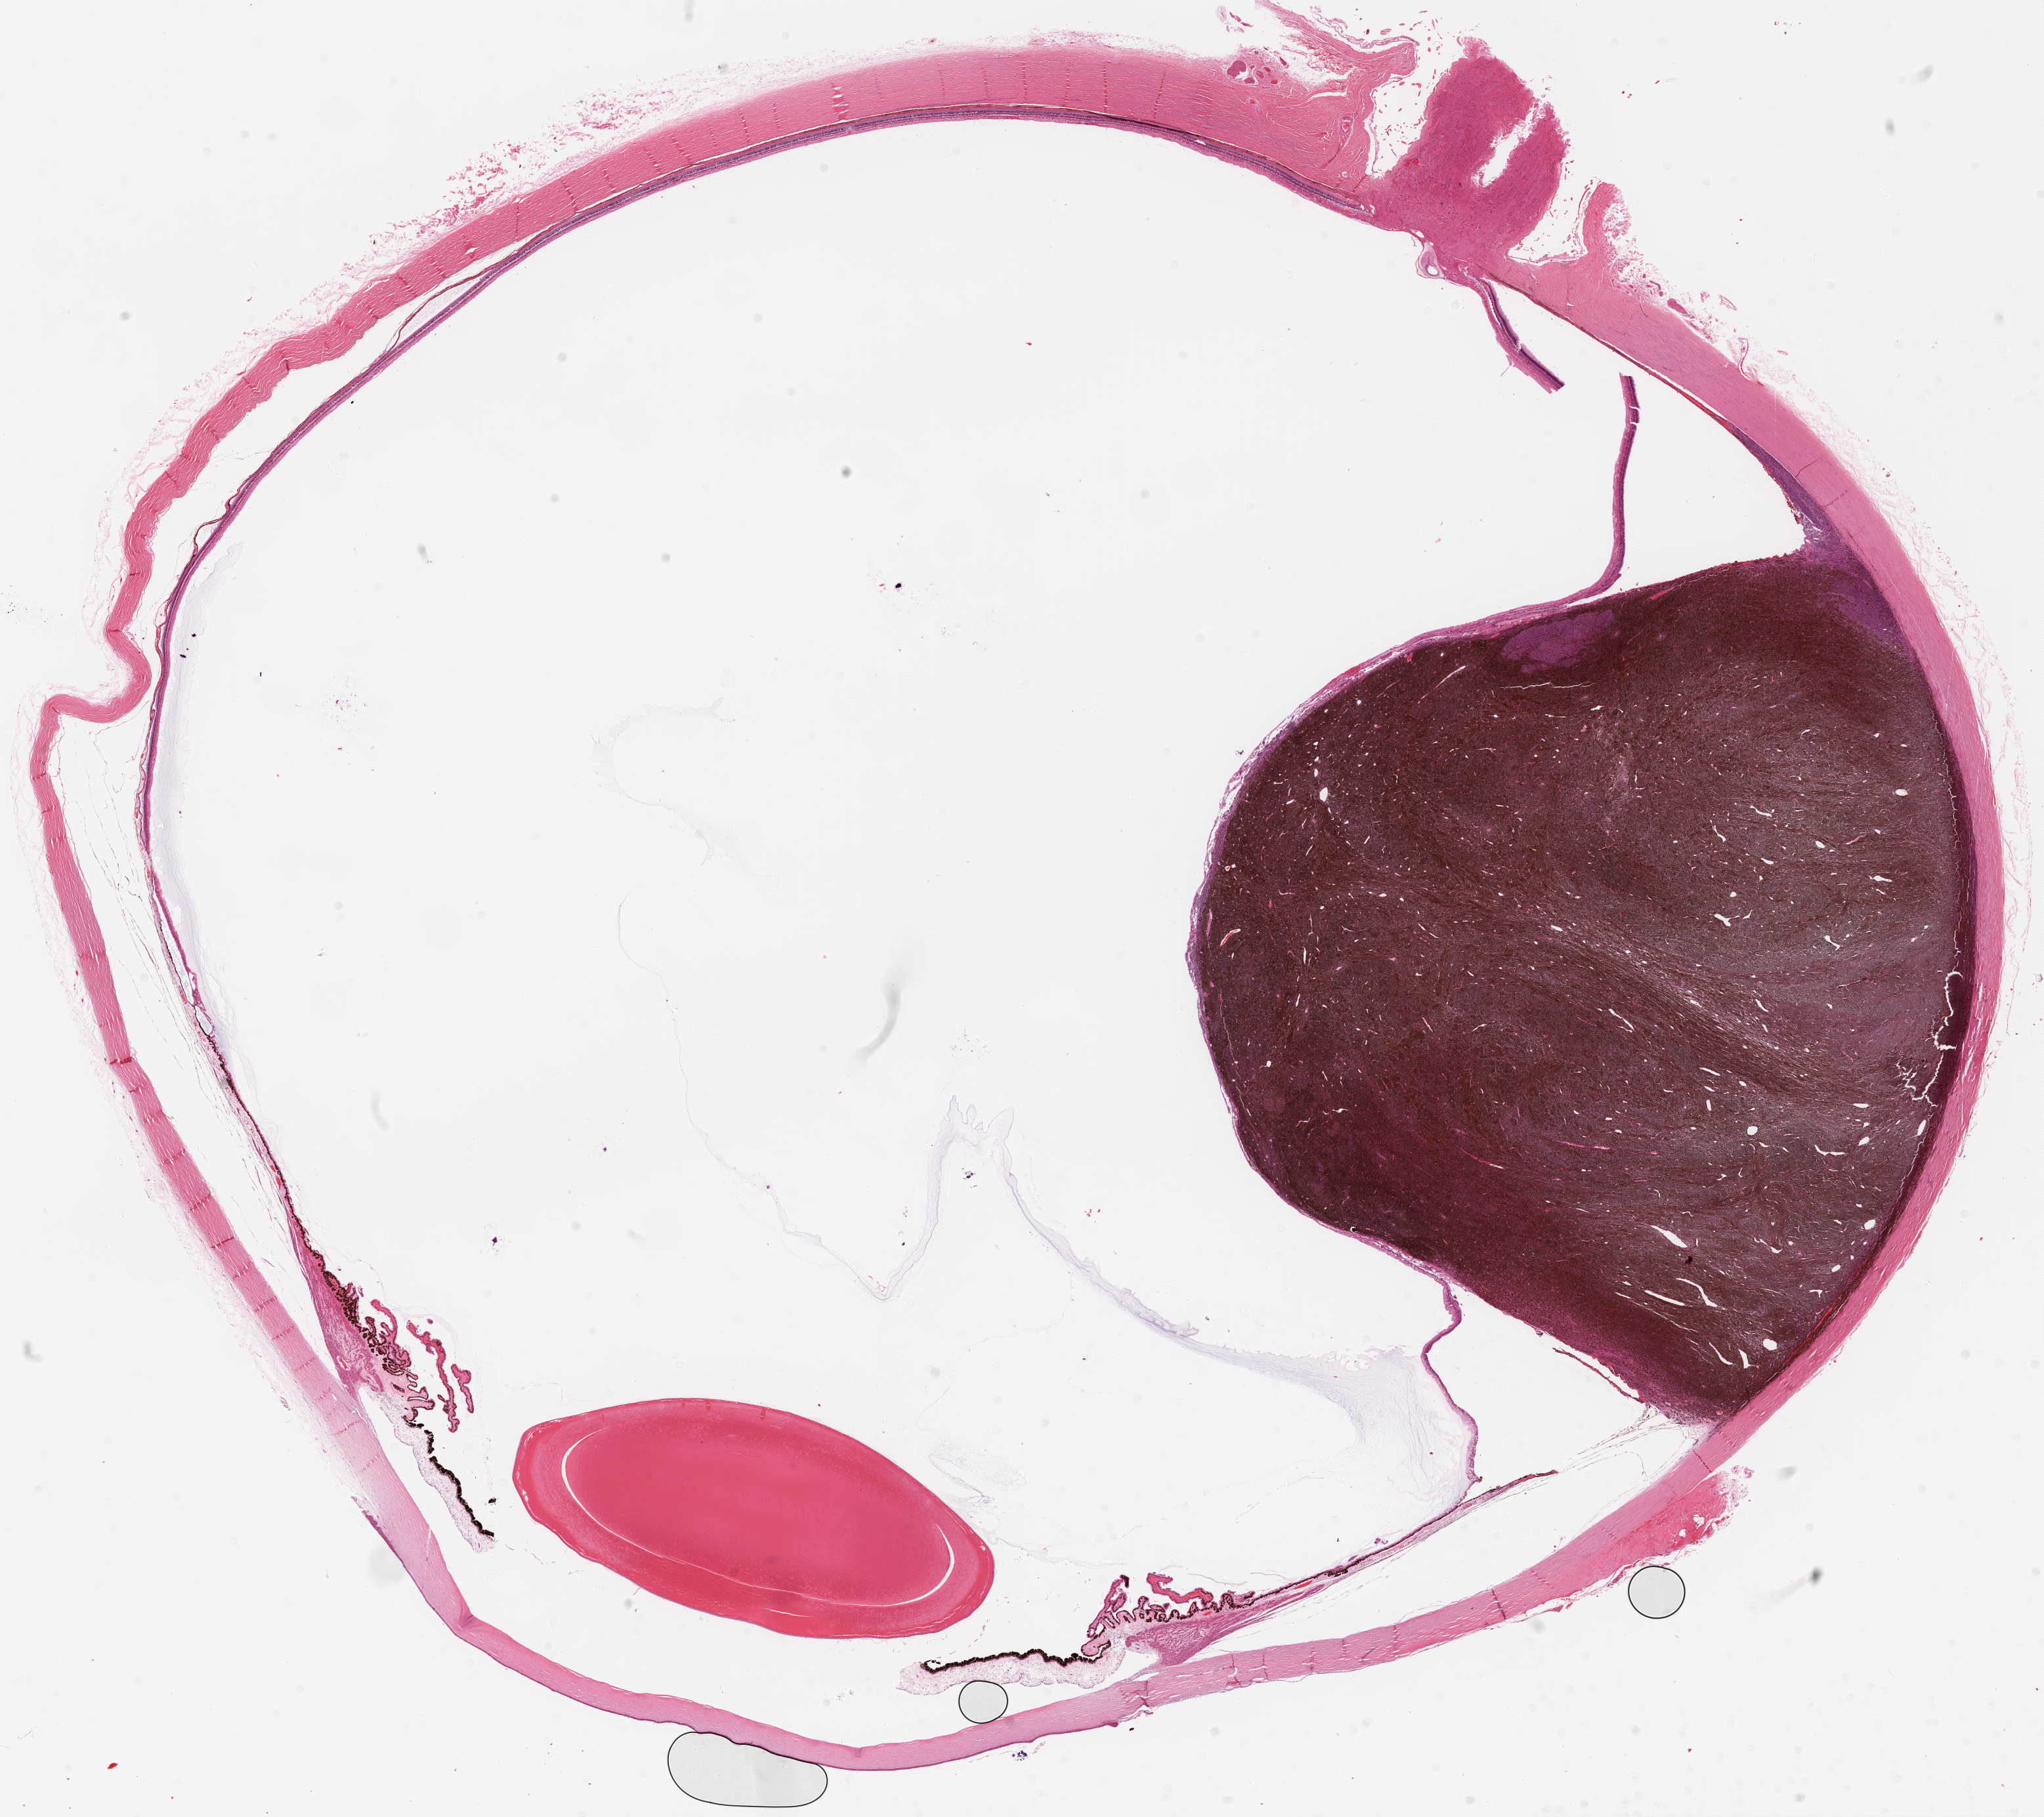
H&E whole-slide image — low-resolution overview of the scanned area, about 25.1 x 22.3 mm, formalin-fixed paraffin-embedded (FFPE) diagnostic section, primary tumour sample from the uvea. Male, age 71 years at initial diagnosis.
Diagnosis: Spindle cell melanoma, type B (choroid).